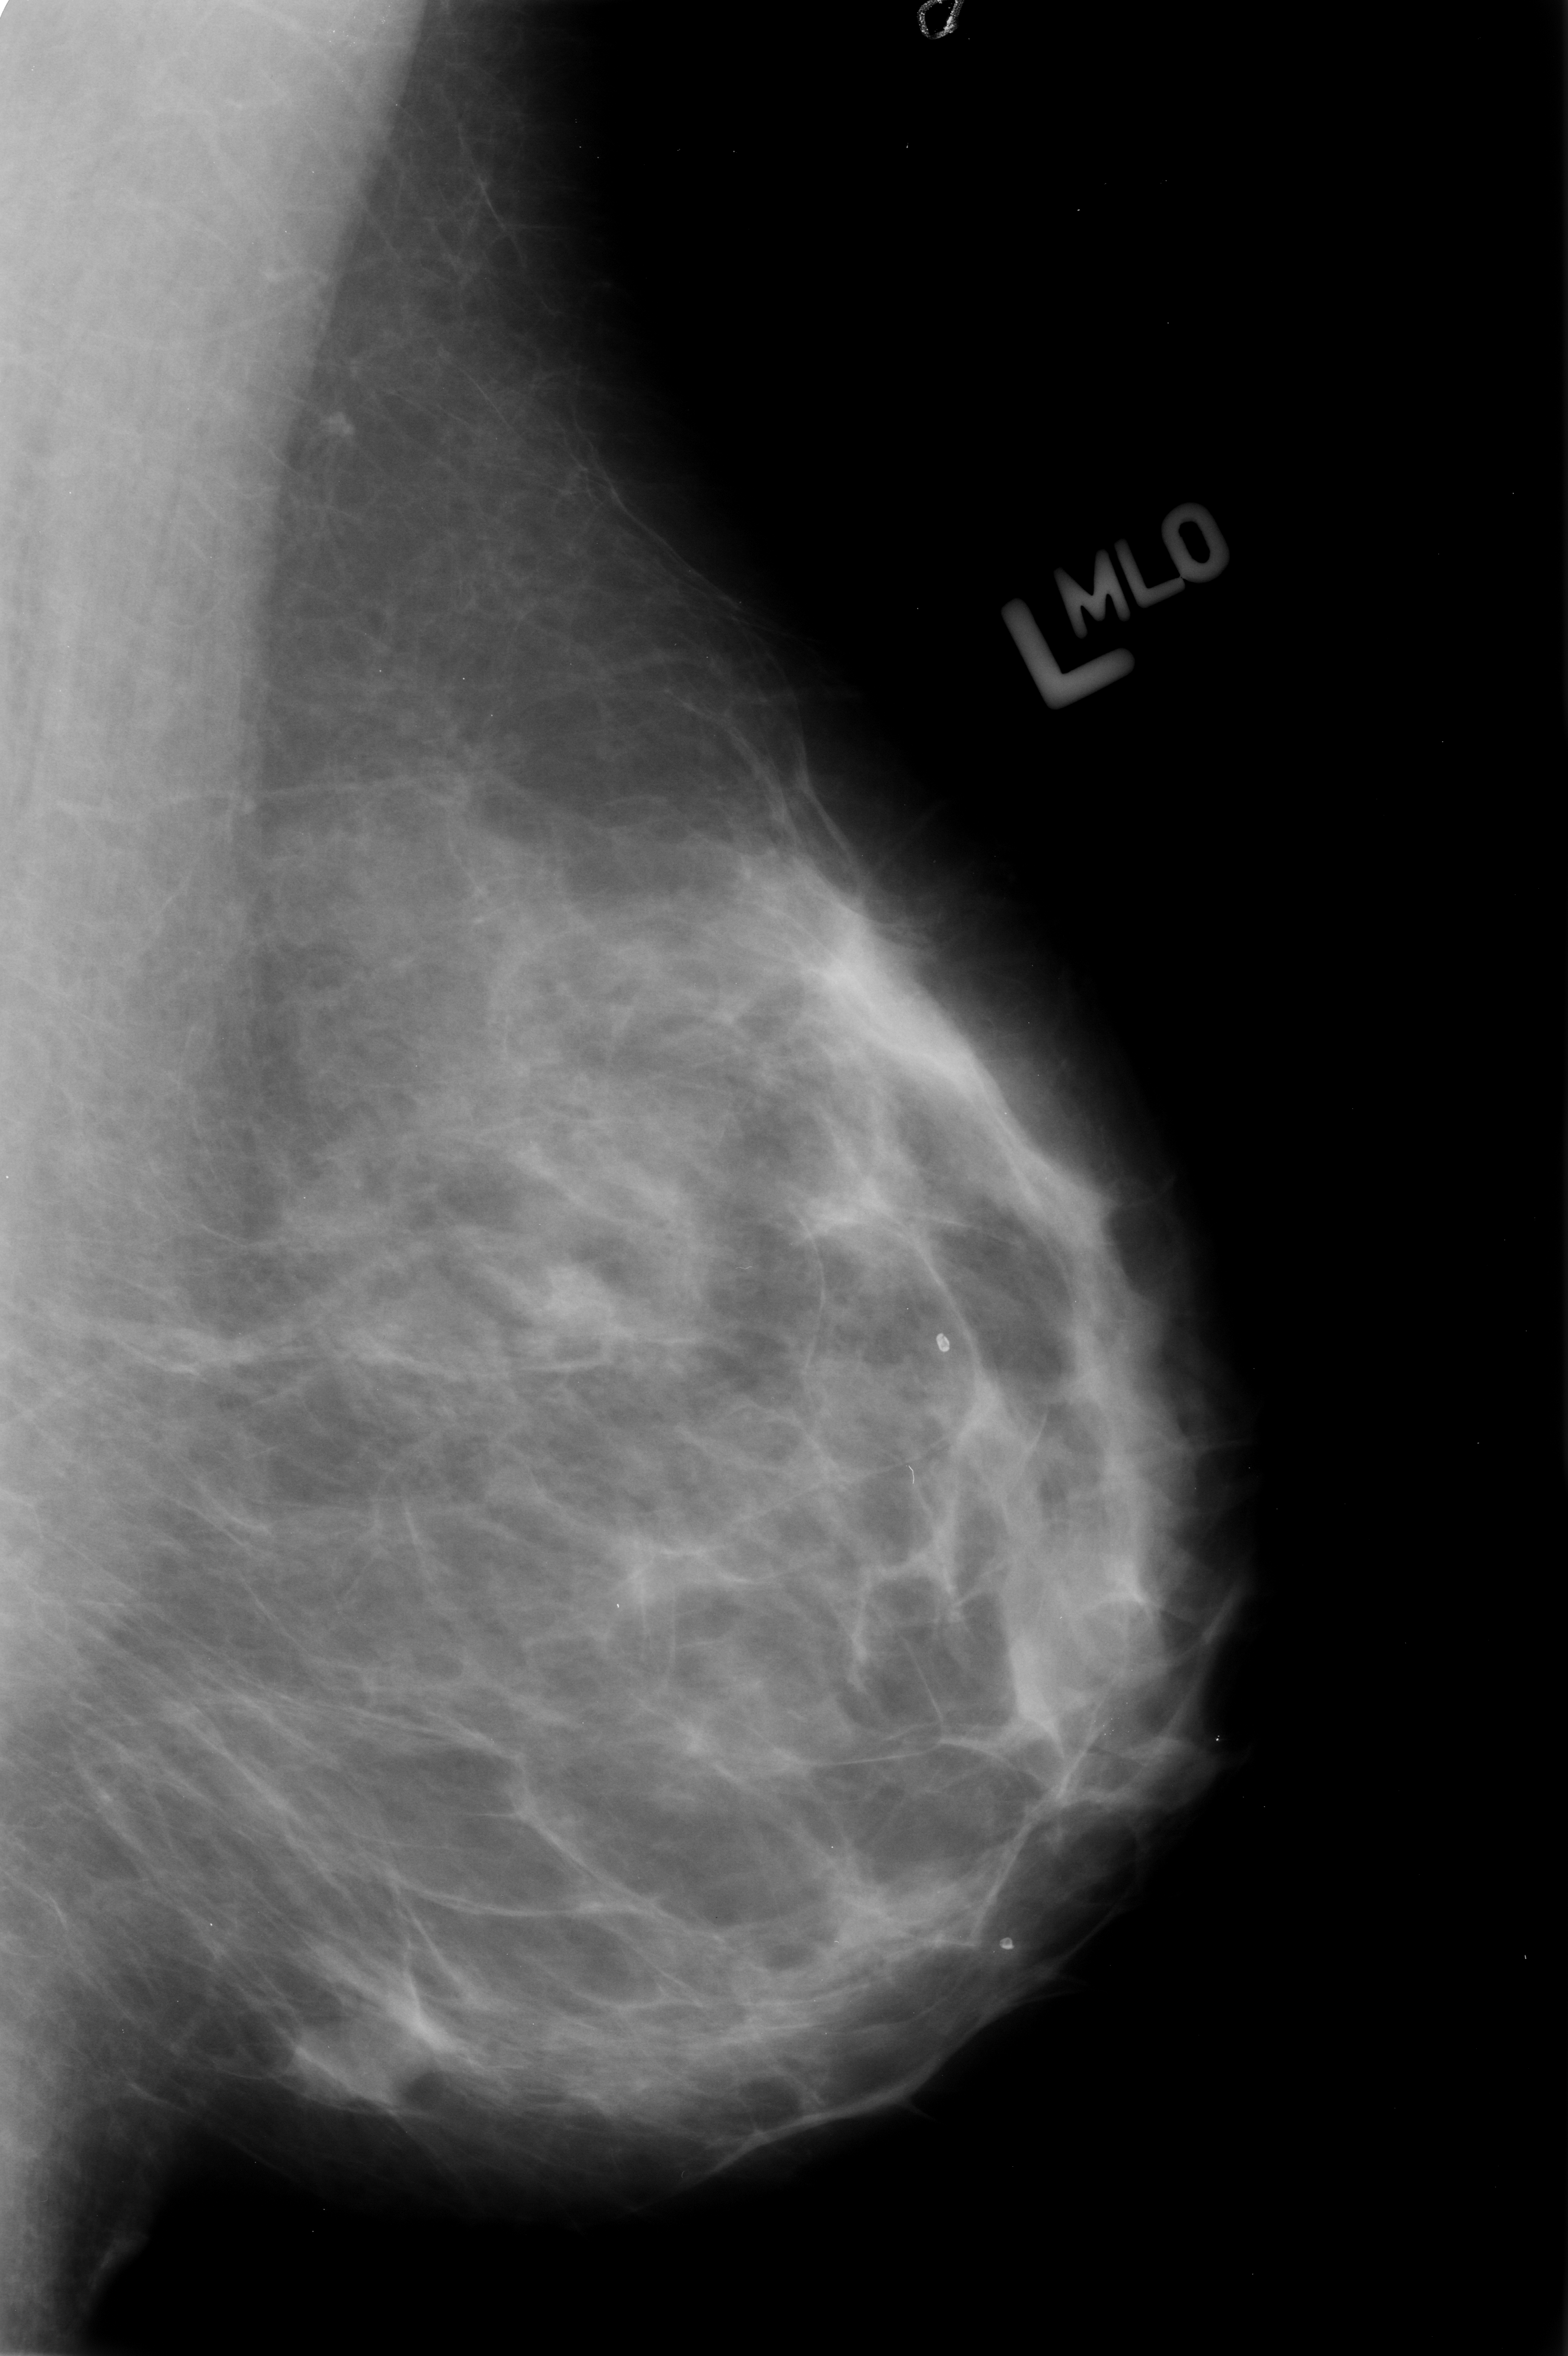
Mammogram (digitized film), left breast, mediolateral oblique (MLO) view, BI-RADS breast density category 2 (scale 1–4).
Mass, shape irregular, margins ill defined; BI-RADS assessment category 4; subtlety rating 3 on a 1 (subtle) to 5 (obvious) scale; pathology result (as recorded, not read from the image): malignant.